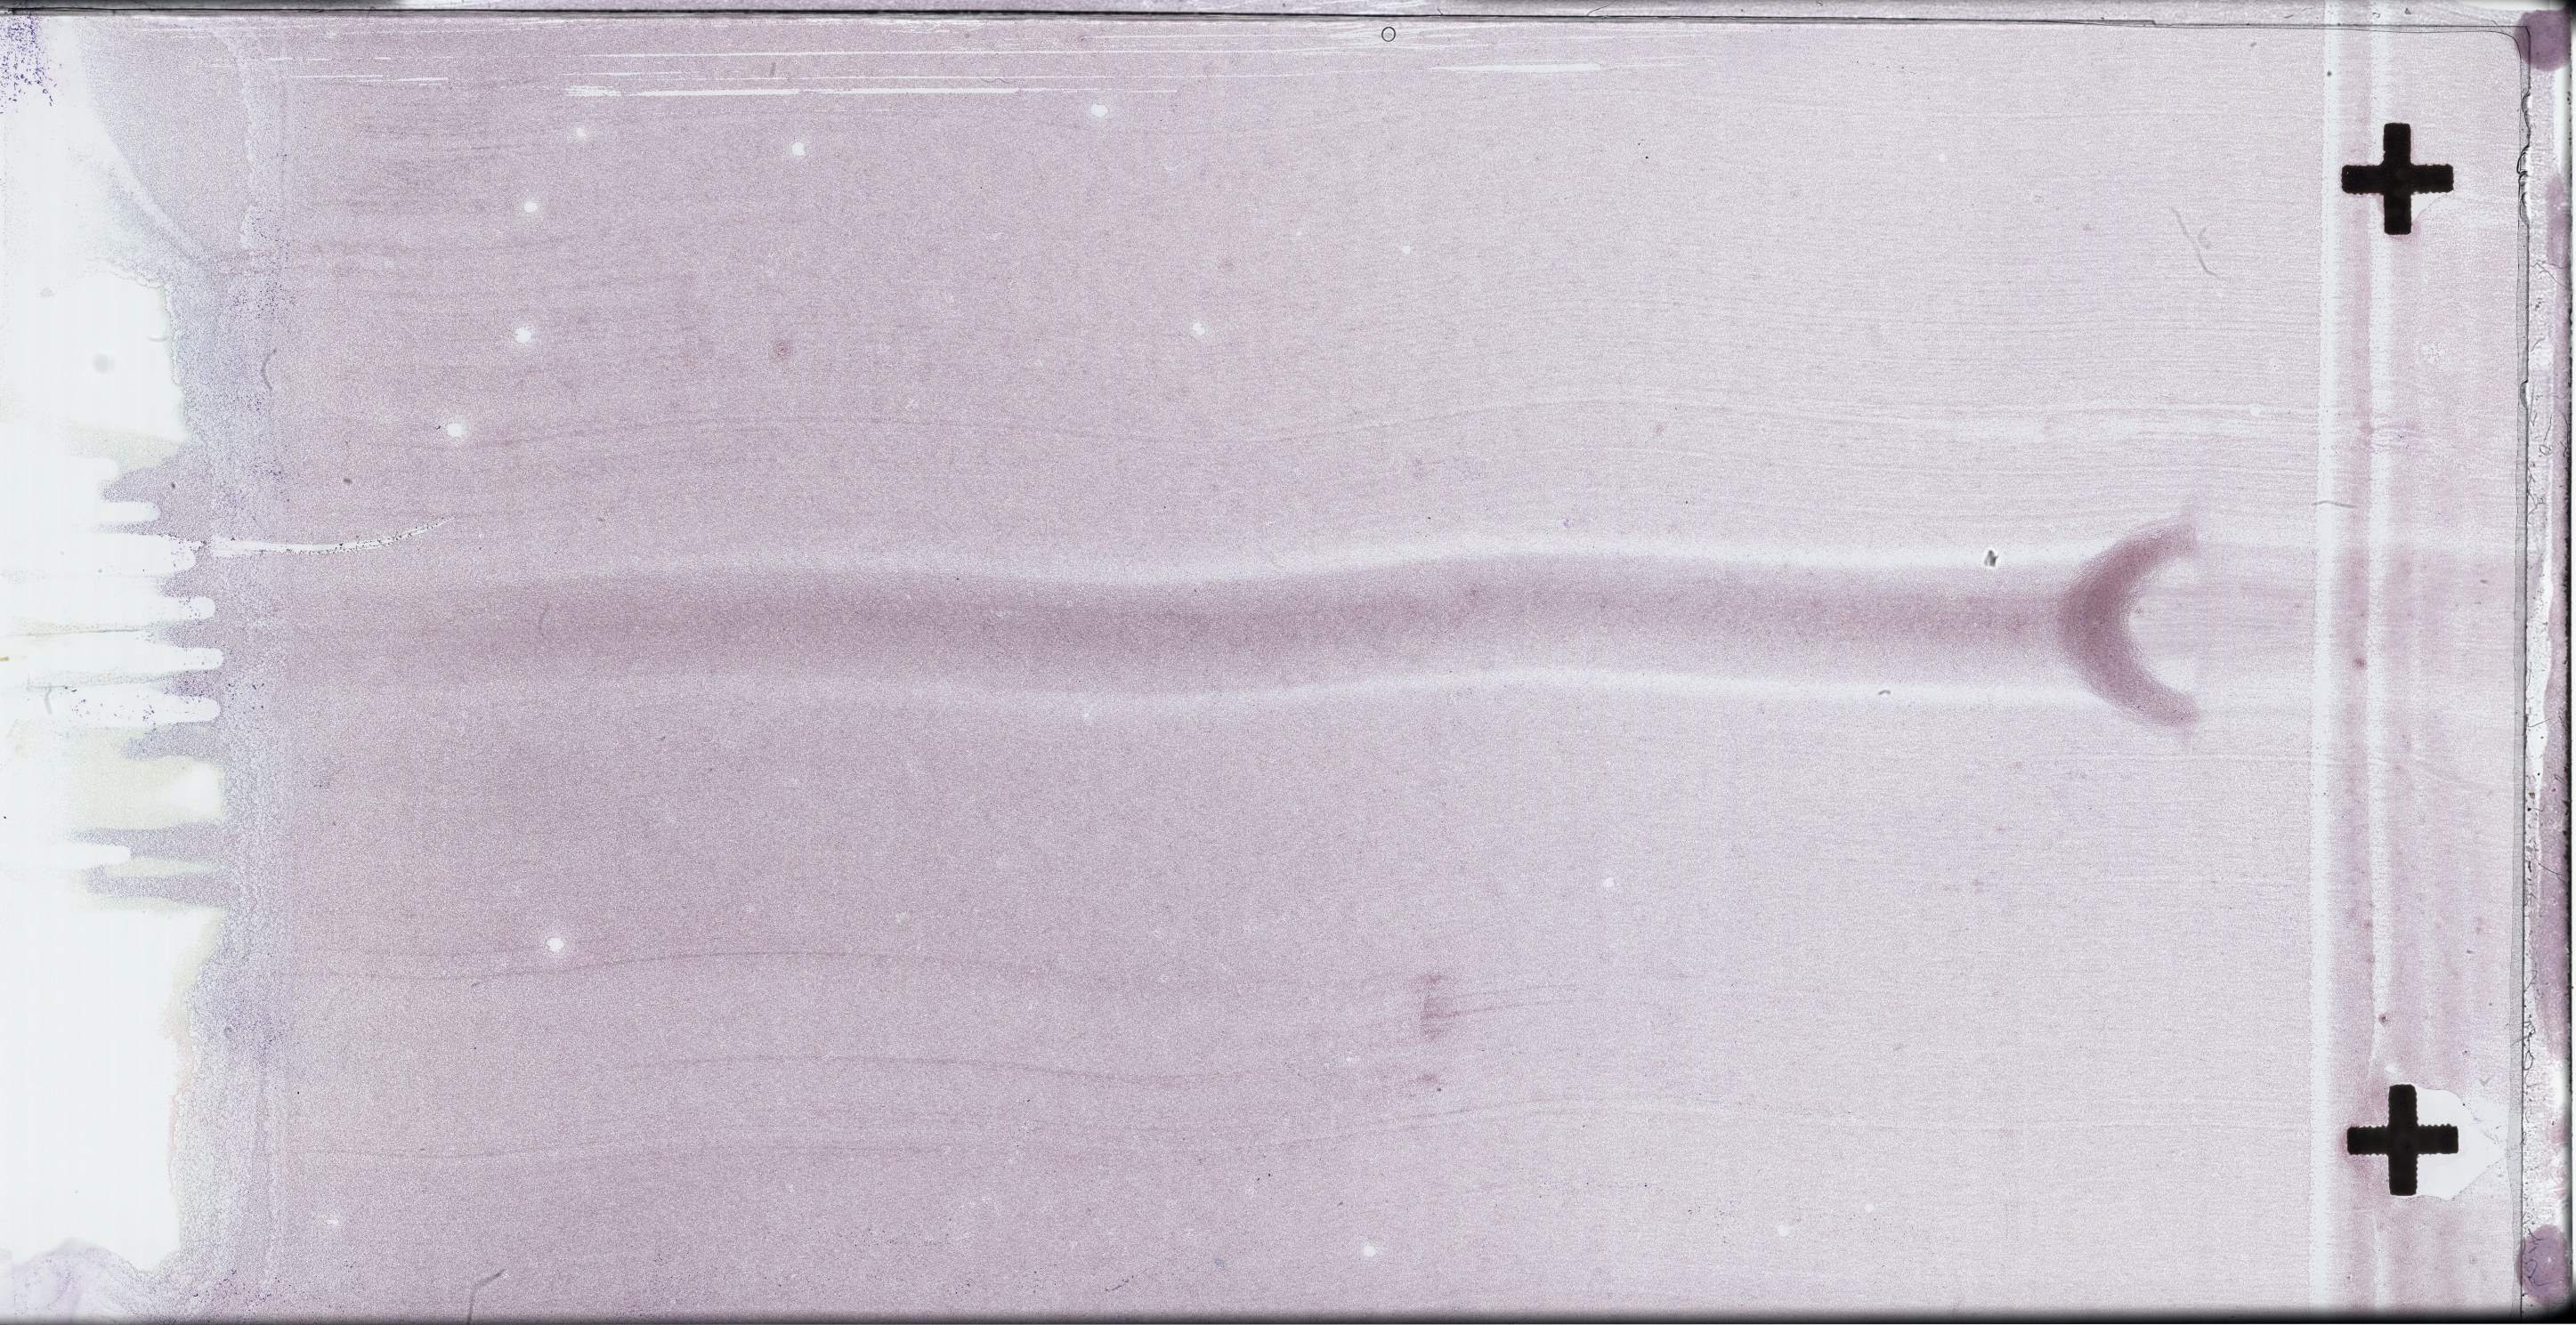
Wright-Giemsa-stained bone marrow smear, whole-slide image — whole scanned area (about 46.7 x 24.0 mm) shown as a low-resolution overview. Patient sex: male.
- from a patient with: Plasma Cell Myeloma